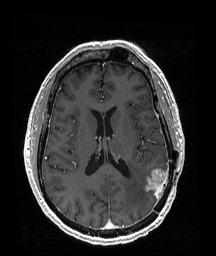
Brain MRI from a brain-tumour surgery series, one axial slice; position 82 of 192 along the scan axis; T1-weighted post-contrast; 1 mm slice thickness; 216 × 256 image matrix. From the clinical record (not read from this slice): histopathology: Glioblastoma; WHO grade: 4; IDH mutation: no.
Annotated regions visible in this slice (expert manual segmentation):
- tumour: bounding box (x1, y1, x2, y2) in pixels: (144, 168, 170, 196)